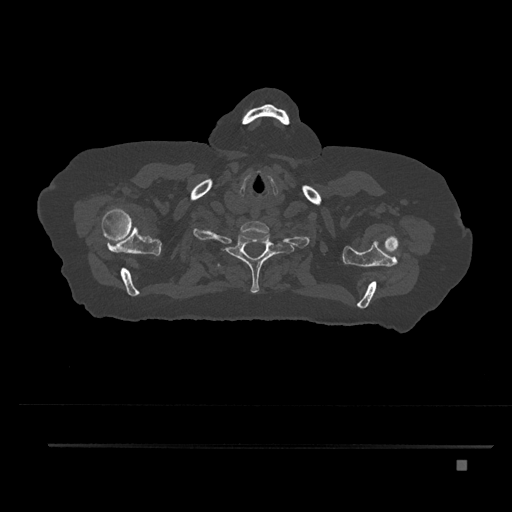
CT including the spine, one axial slice. Slice 701 of 797 in the series (ordered by position). 120 kVp. Bone window (W 1800 / L 400 HU). 0.5 mm slice thickness. 512 × 512 image matrix, field of view 437 × 437 mm. Patient: female, 76 years. From the clinical record (not read from this slice): primary cancer: lung.
Structures marked on this image (semi-automatically segmented with operator editing):
- T1 vertebra: bounding box [x1, y1, x2, y2] px = [225, 232, 283, 293]
- T2 vertebra: [218, 247, 229, 267]